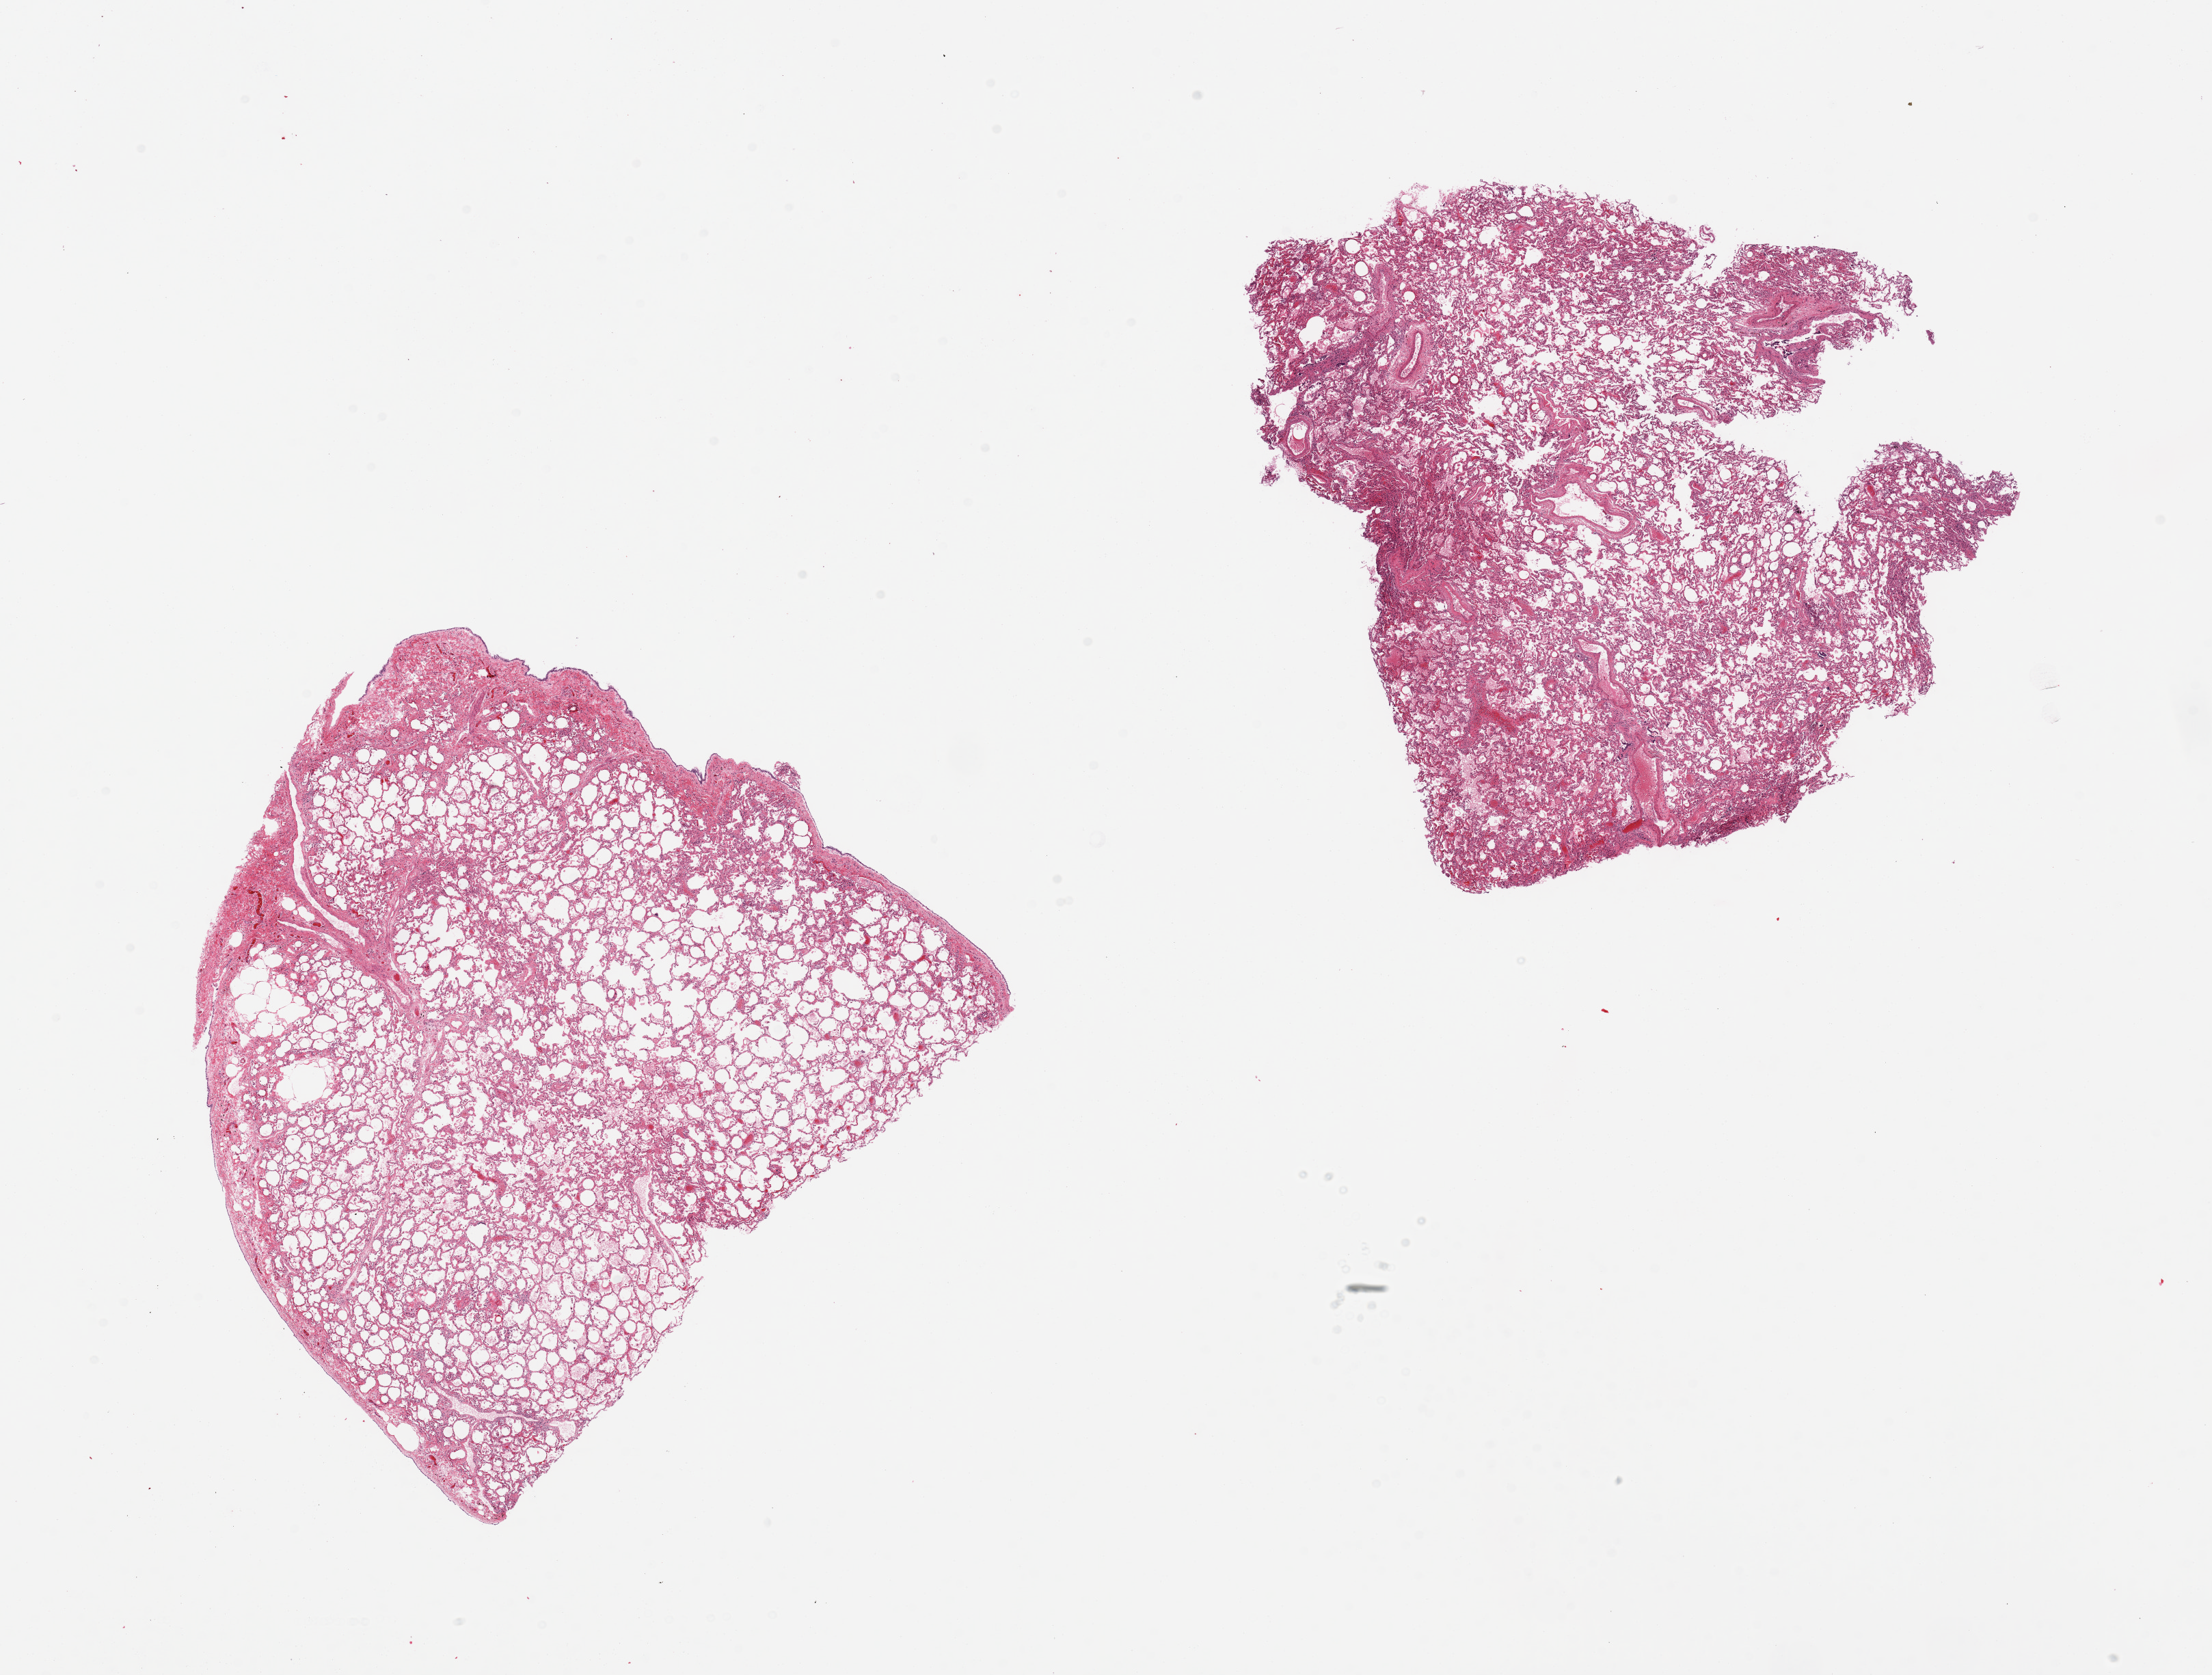
H&E whole-slide image, brightfield, low-resolution overview of the scanned area, about 25.6 x 19.4 mm (from a 20x scan), PAXgene-fixed, paraffin-embedded tissue, sampled site (target tissue): lung, tissue donor sample. Donor: female.
Review note (as recorded): 2 pieces; pleura [not target] along 1 surface.